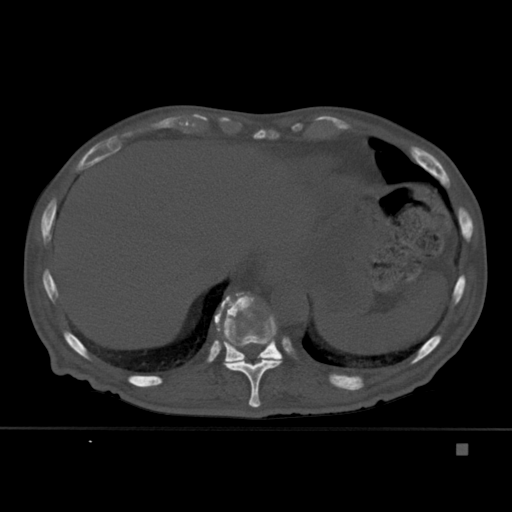
CT including the spine, one axial slice. Slice 226 of 451 in the series (ordered by position). Bone window (W 1800 / L 400 HU). 512 × 512 image matrix, field of view 378 × 378 mm. Patient: male, 75 years. From the clinical record (not read from this slice): primary cancer: prostate.
Structures marked on this image (semi-automatic segmentation, software-assisted and operator-edited):
- T10 vertebra: bounding box (x1, y1, x2, y2) in pixels: (216, 293, 282, 408)
- T11 vertebra: (214, 292, 288, 363)